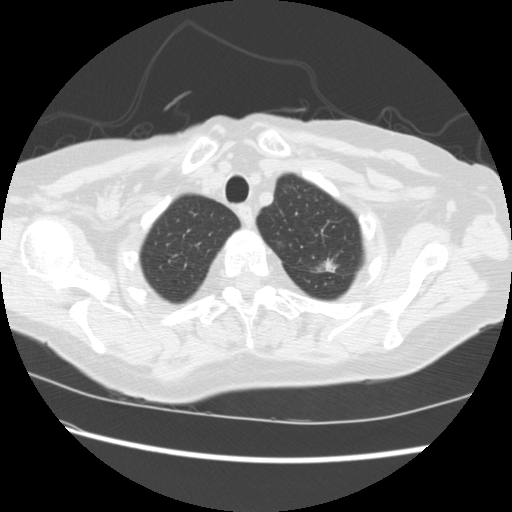
Low-dose screening chest CT, one axial slice; position 191 of 224 along the scan axis; 120 kVp; lung window (W 1500 / L -600 HU); 2.5 mm slice thickness; 512 × 512 image matrix, field of view 340 × 340 mm.
Outlined on this slice (expert manual segmentation):
- lesion 1 (tumor, upper lobe of left lung): bounding box <322,260,336,272> (left, top, right, bottom; pixels)